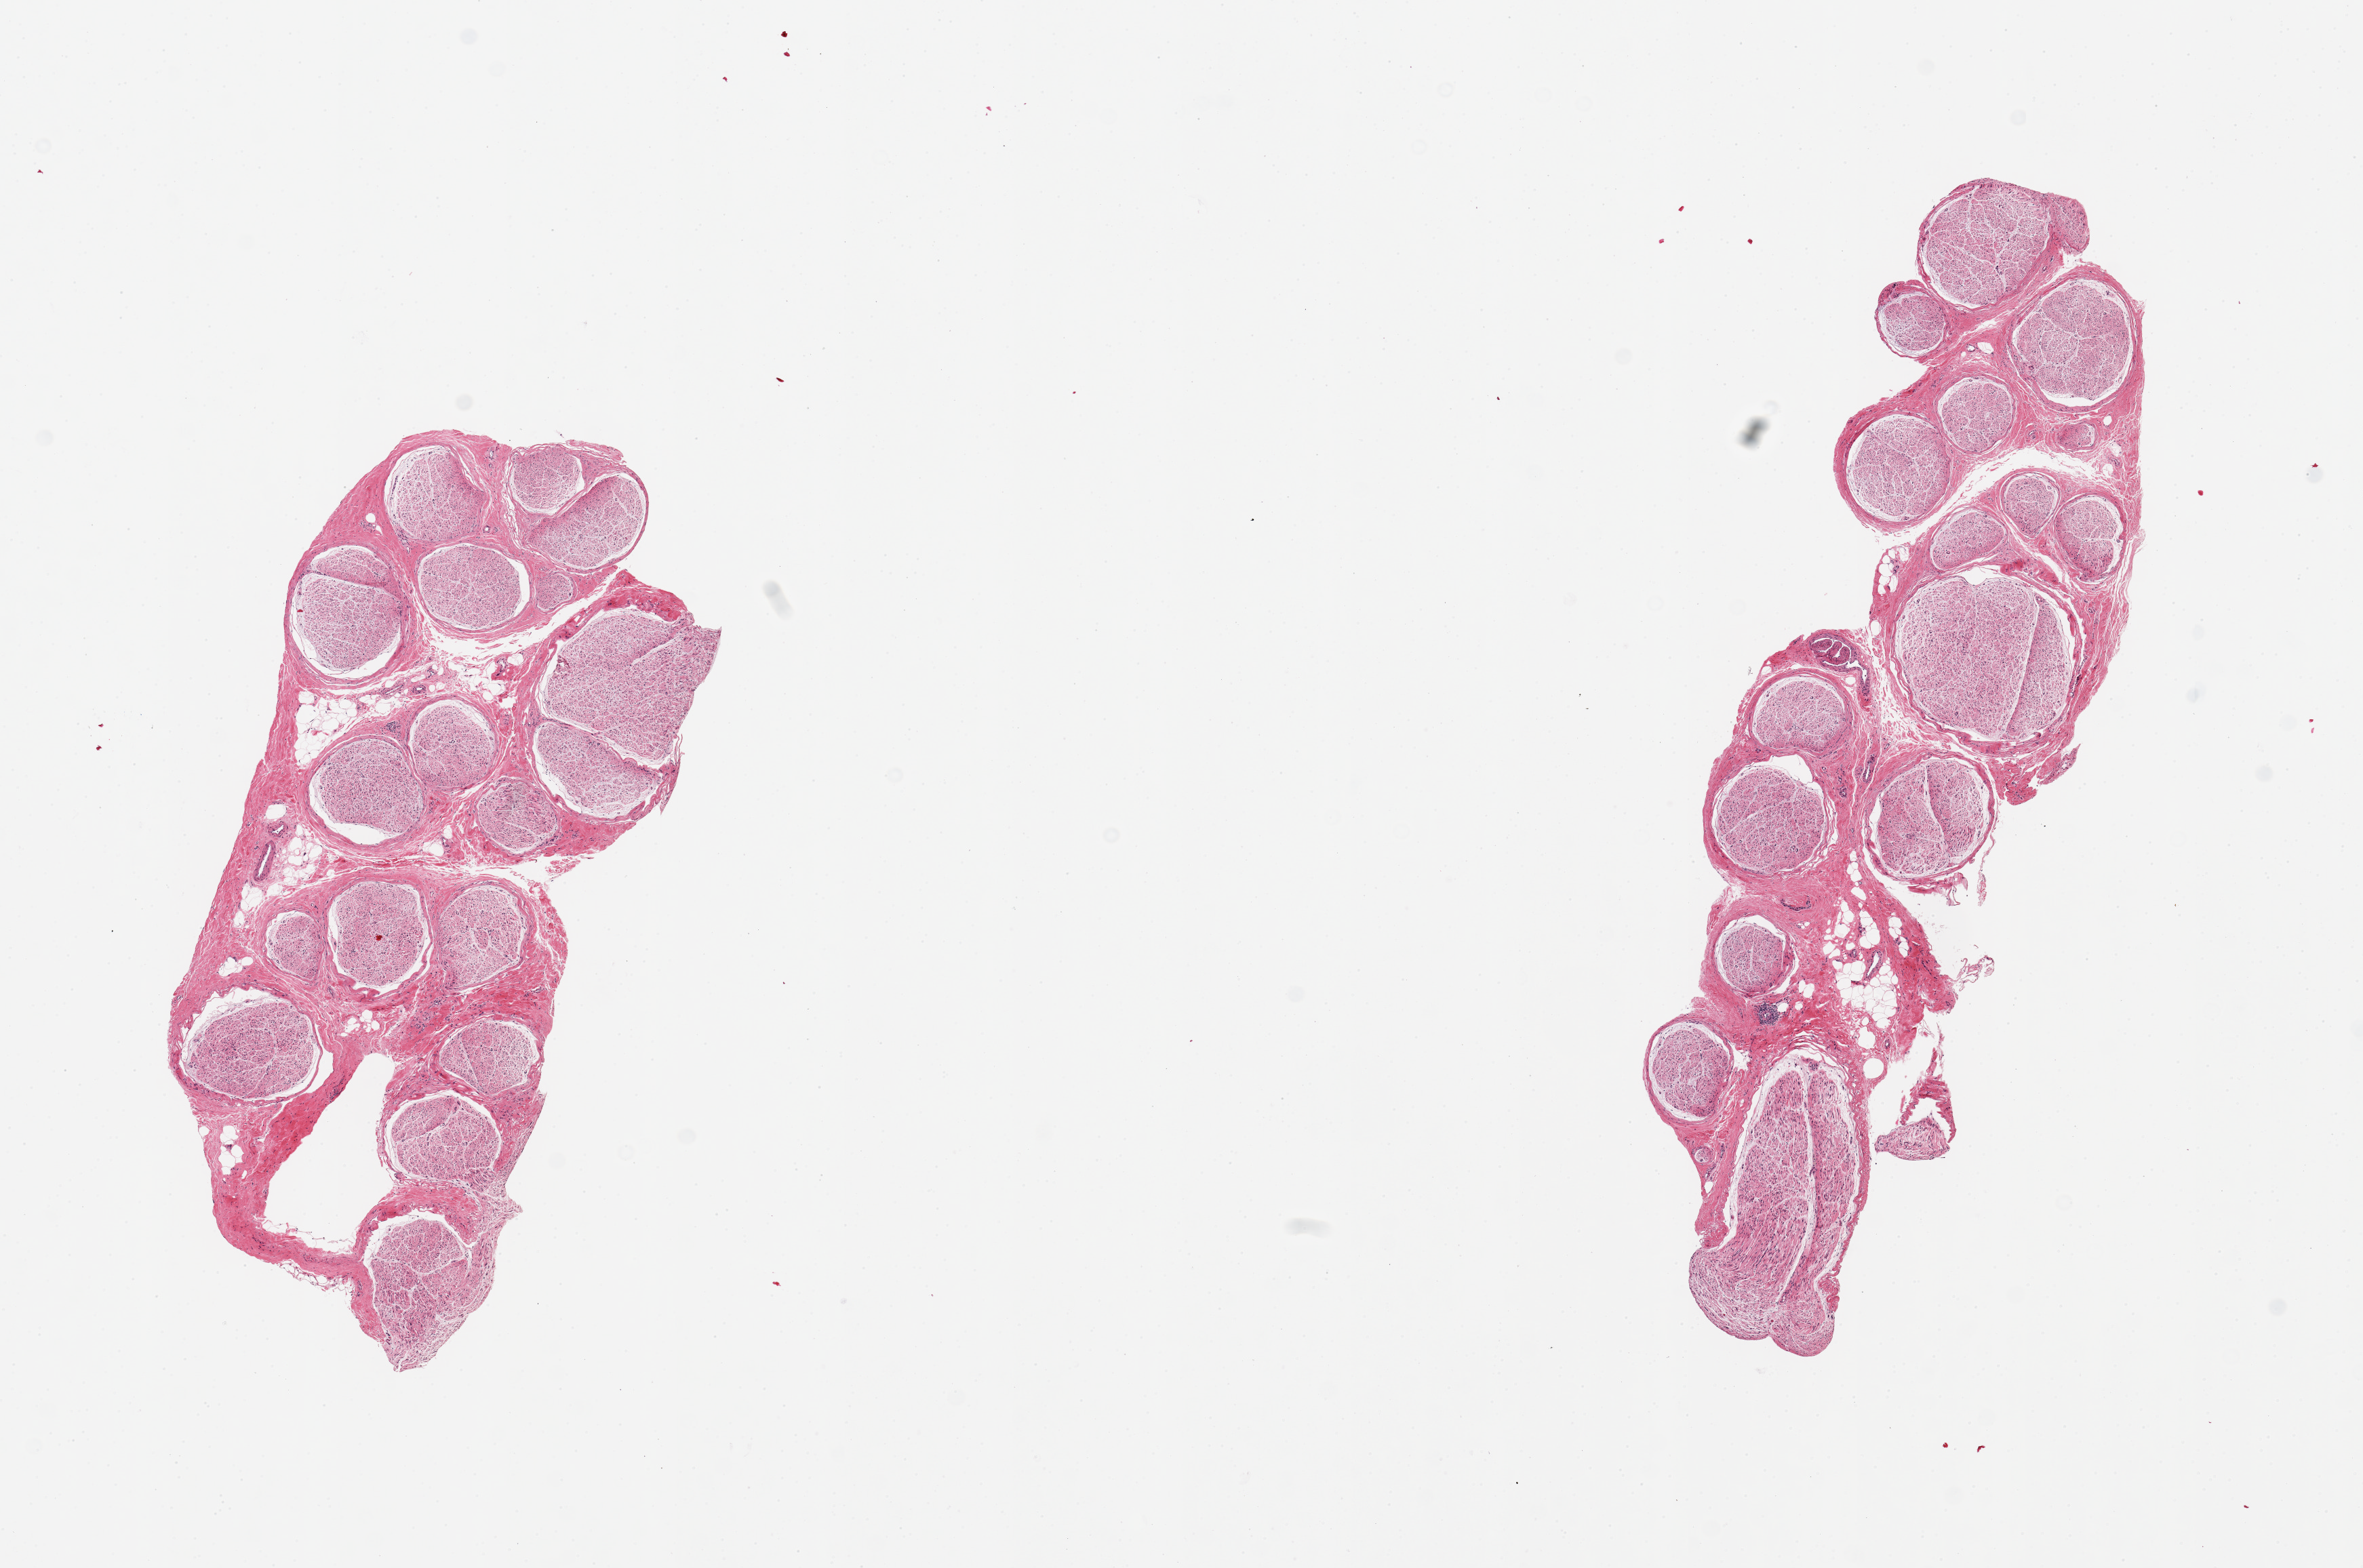
Digitized haematoxylin and eosin-stained section, whole scanned area (about 13.8 x 9.1 mm, slide scanned at 20x) shown as a low-resolution overview. PAXgene-fixed, paraffin-embedded tissue. Target tissue: tibial nerve. Tissue donor sample. Donor sex: male.
Pathologist's review note for this sample: 2 pieces; 10% internal fat.